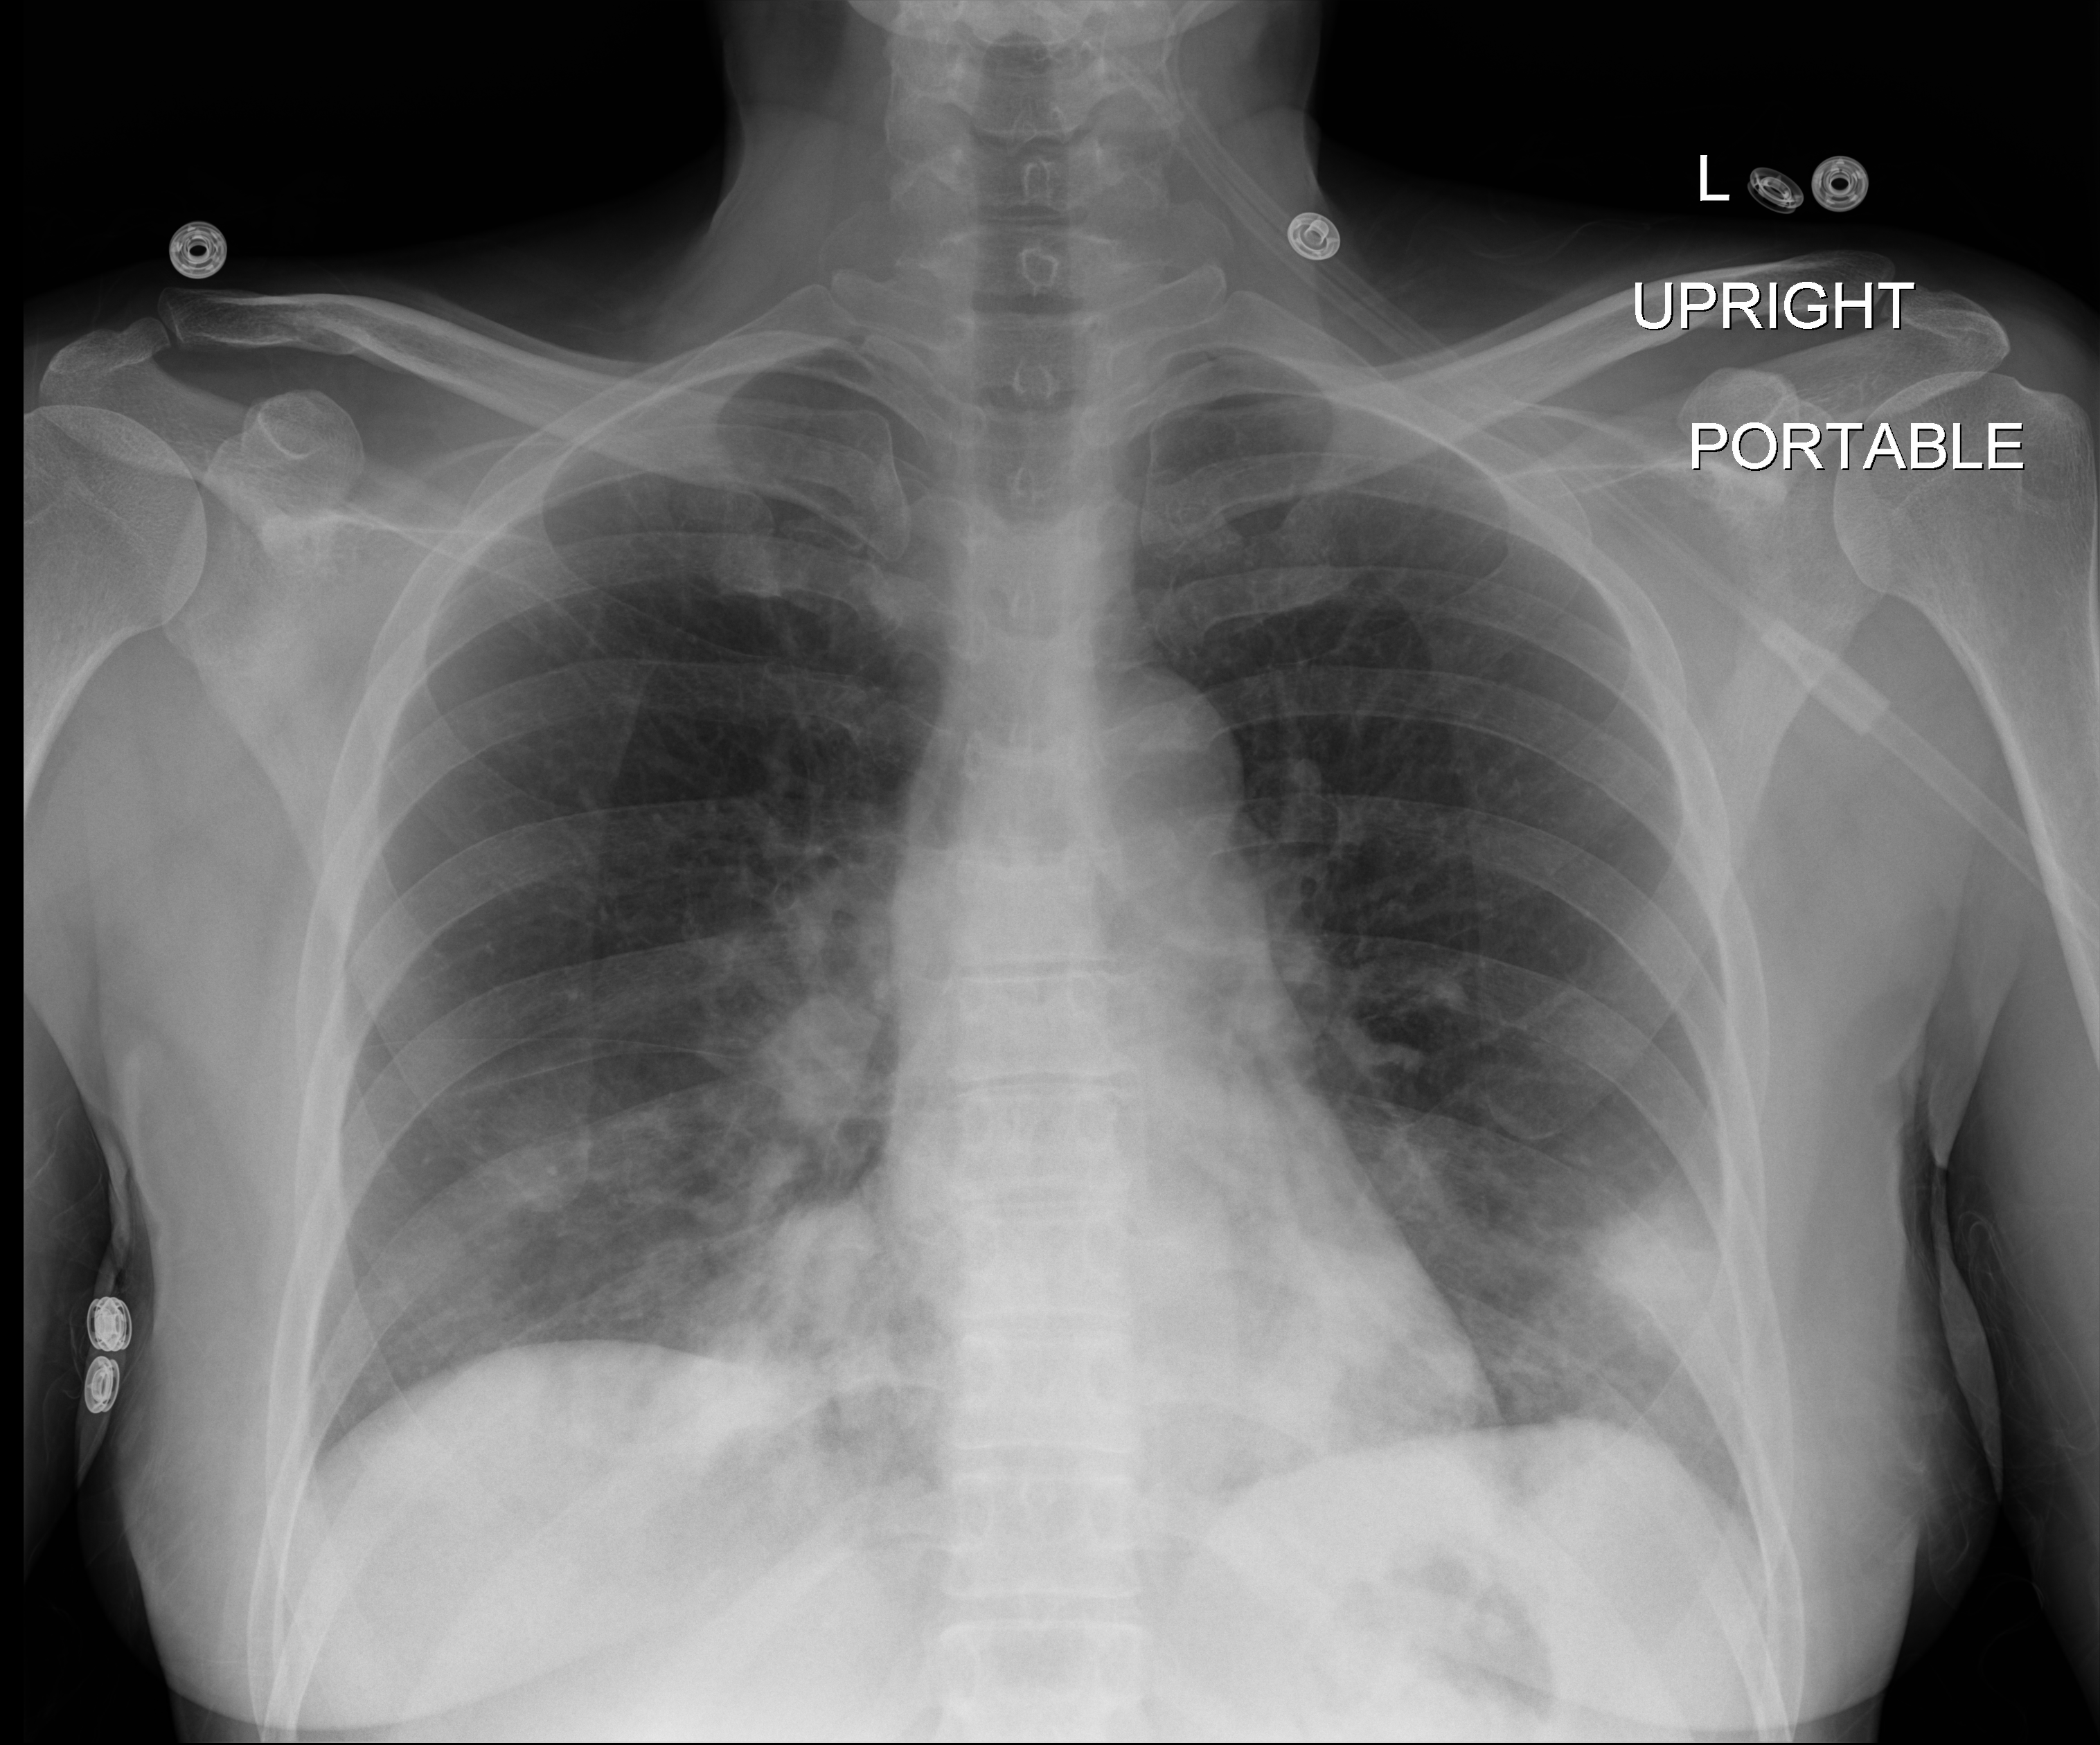
Portable chest radiograph; anteroposterior (AP) projection. Patient hospitalised with COVID-19; female, aged 18–59 years.
Hospital-stay facts (about this admission, not read from this image; timing relative to this image not recorded): admitted to intensive care during this hospital stay: yes; mechanically ventilated during this hospital stay: no; hypertension (admission record): no.